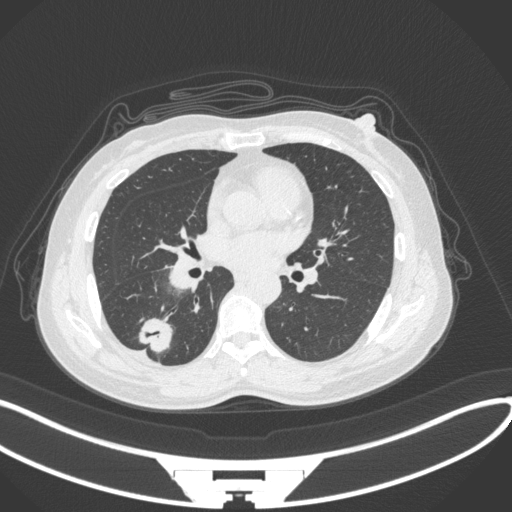
Chest CT, one axial slice. Position 149 of 352 along the scan axis. Reconstruction kernel B31f. 120 kVp. Lung window (W 1500 / L -600 HU). 1 mm slice thickness. 512 × 512 image matrix, field of view 400 × 400 mm. Patient: female, 55 years. Case-level facts recorded for this patient, not image findings: clinical TNM (as recorded): T1c N1 M0.
Annotated regions visible in this slice (bounding box drawn by a radiologist):
- lung tumour (recorded histology: adenocarcinoma): bounding box <132,316,177,354> (left, top, right, bottom; pixels)